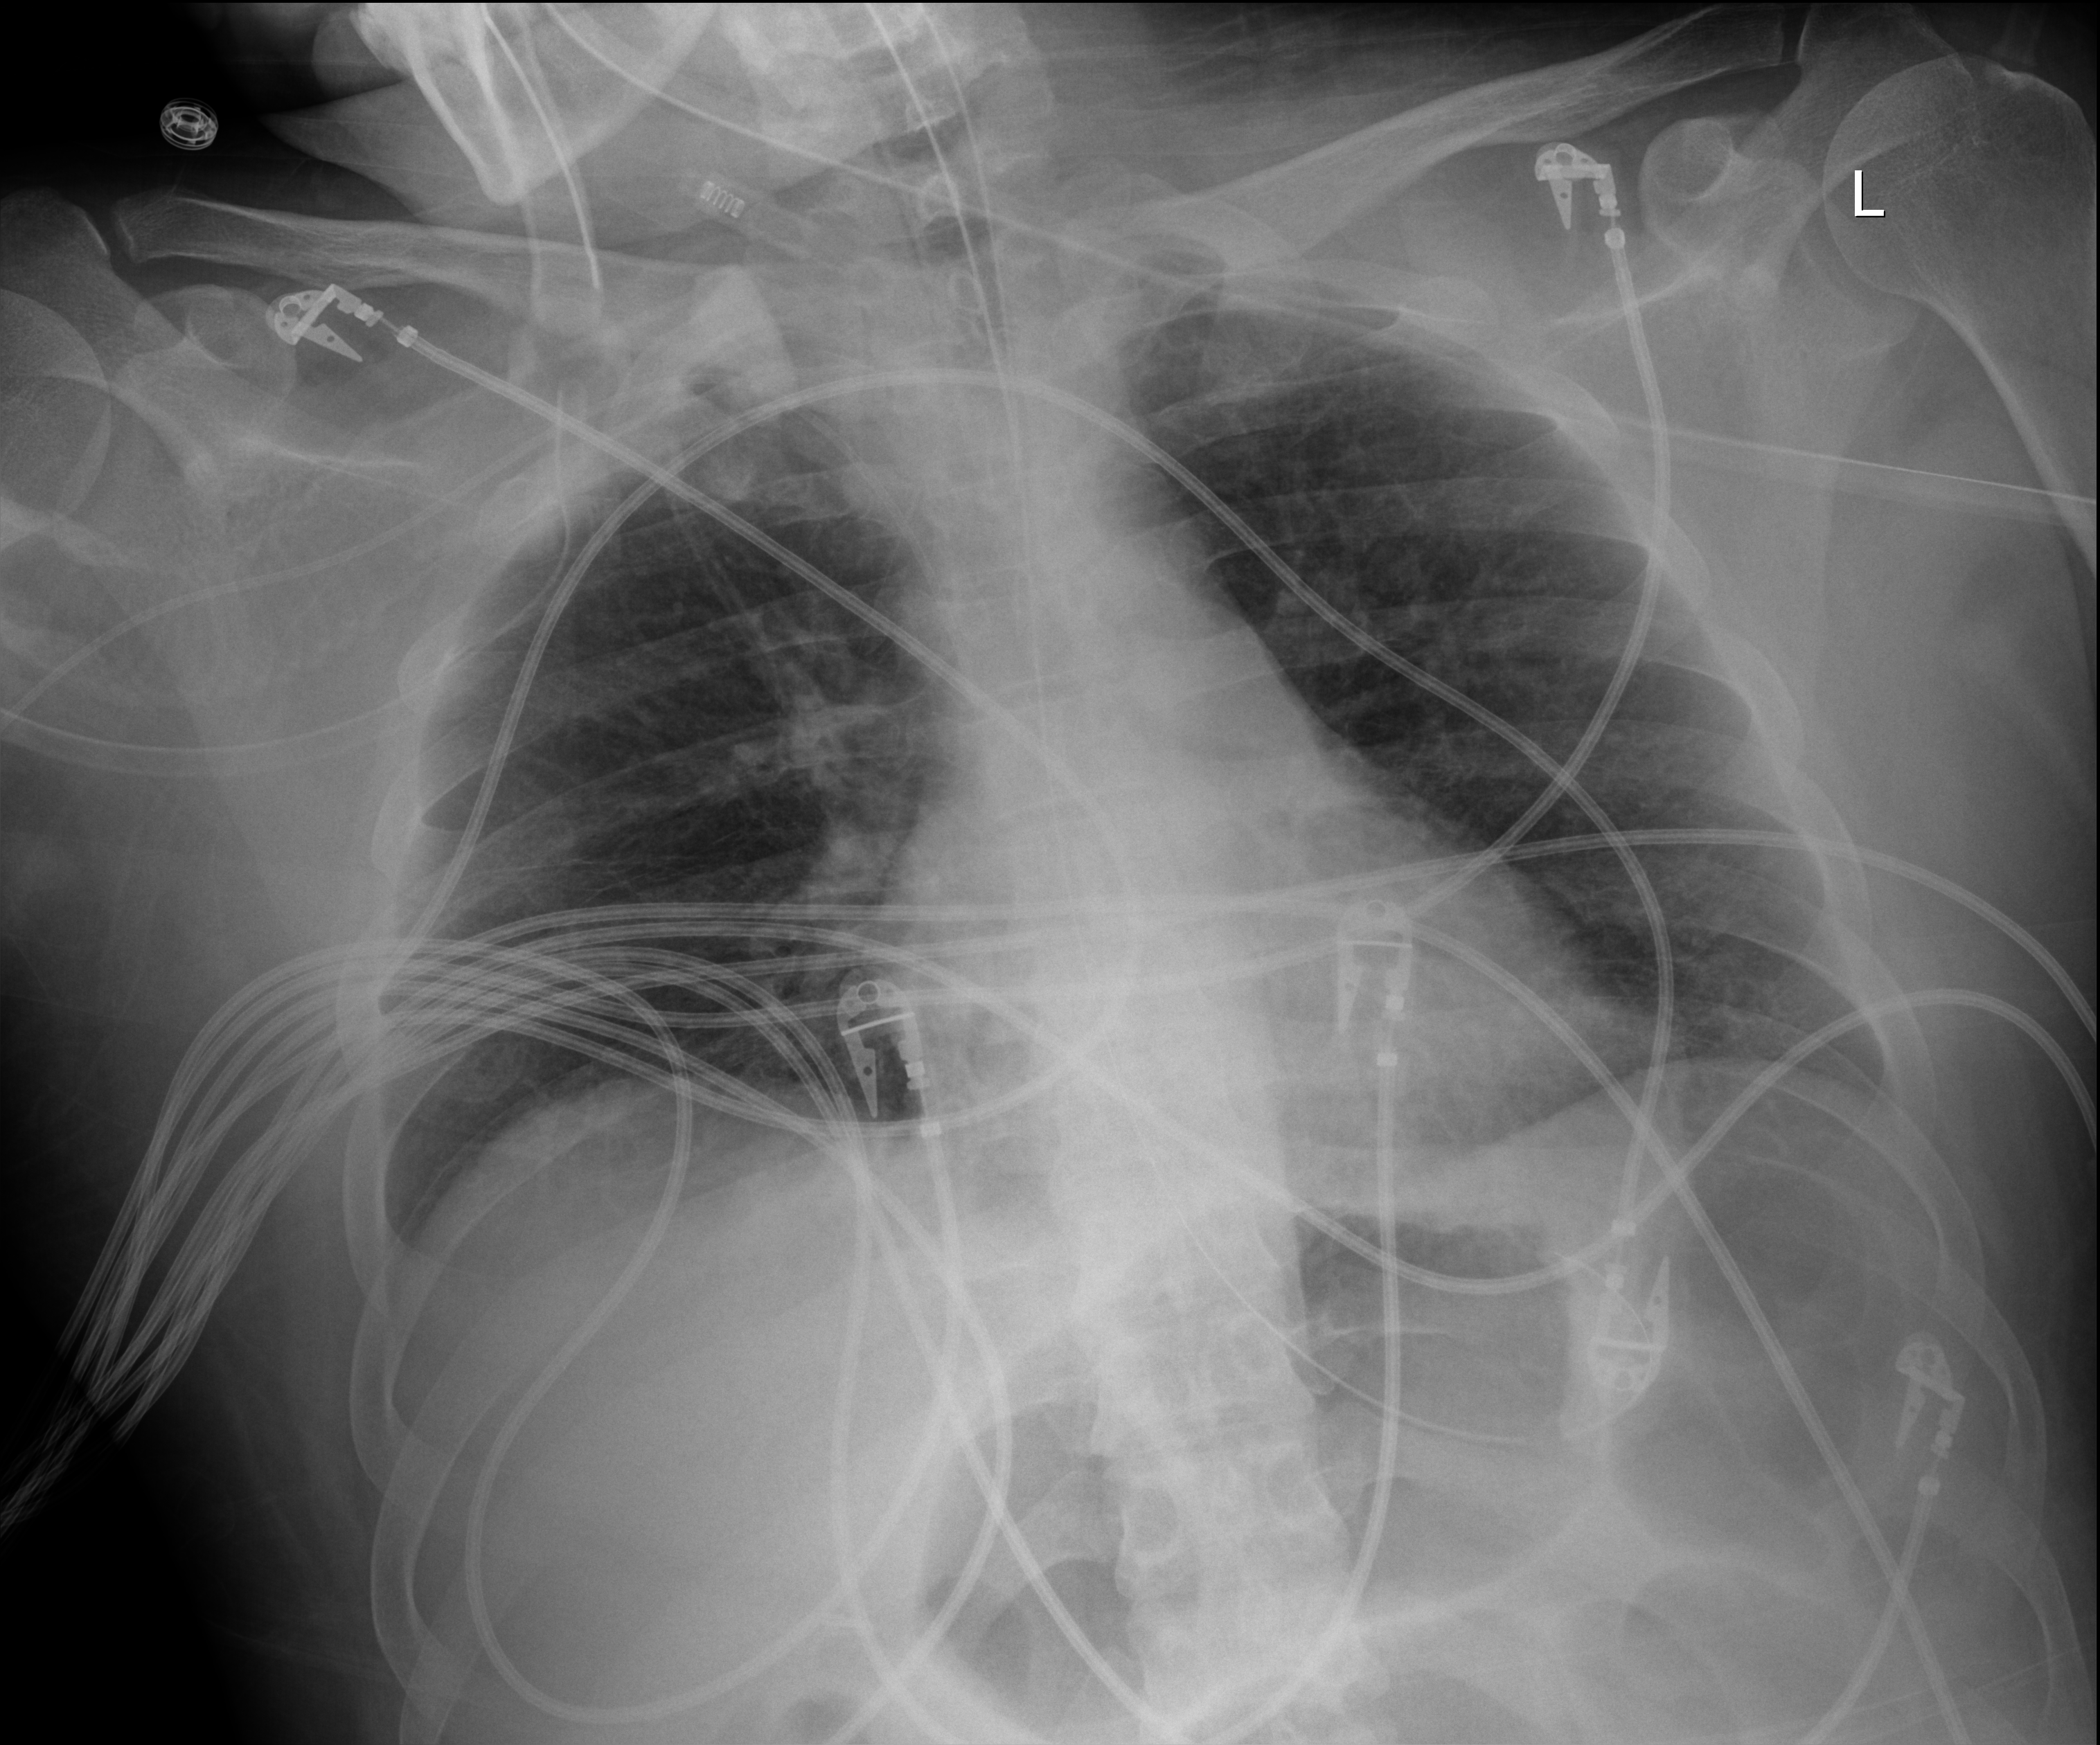
Chest X-ray (portable); anteroposterior (AP) projection. Male patient hospitalised with COVID-19, age 18–59 years.
Hospital-stay facts (about this admission, not read from this image; timing relative to this image not recorded): other chronic lung disease (admission record): no; mechanically ventilated during this hospital stay: yes; admitted to intensive care during this hospital stay: yes.